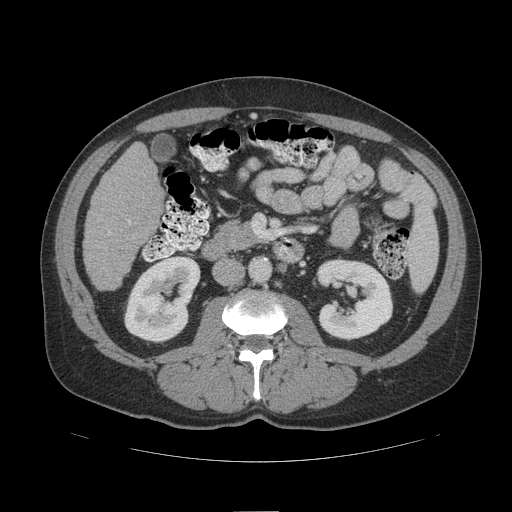
Contrast-enhanced abdominal CT (liver protocol), one axial slice. Position 38 of 109 along the scan axis. 140 kVp. Soft-tissue window (W 400 / L 40 HU). 512 × 512 image matrix, field of view 420 × 420 mm. From the clinical record (not read from this slice): diagnosis: hepatocellular carcinoma (patient treated with transarterial chemoembolisation; whether this scan precedes or follows treatment is not stated here); TNM stage (as recorded): Stage-IIIB; Child-Pugh class: A.
Structures marked on this image (semi-automatic segmentation, software-assisted and operator-edited):
- liver parenchyma outside the tumour (the mass and vessels are separate outlines, so this box may not span the whole liver): bounding box (x1, y1, x2, y2) in pixels: (84, 142, 164, 290)